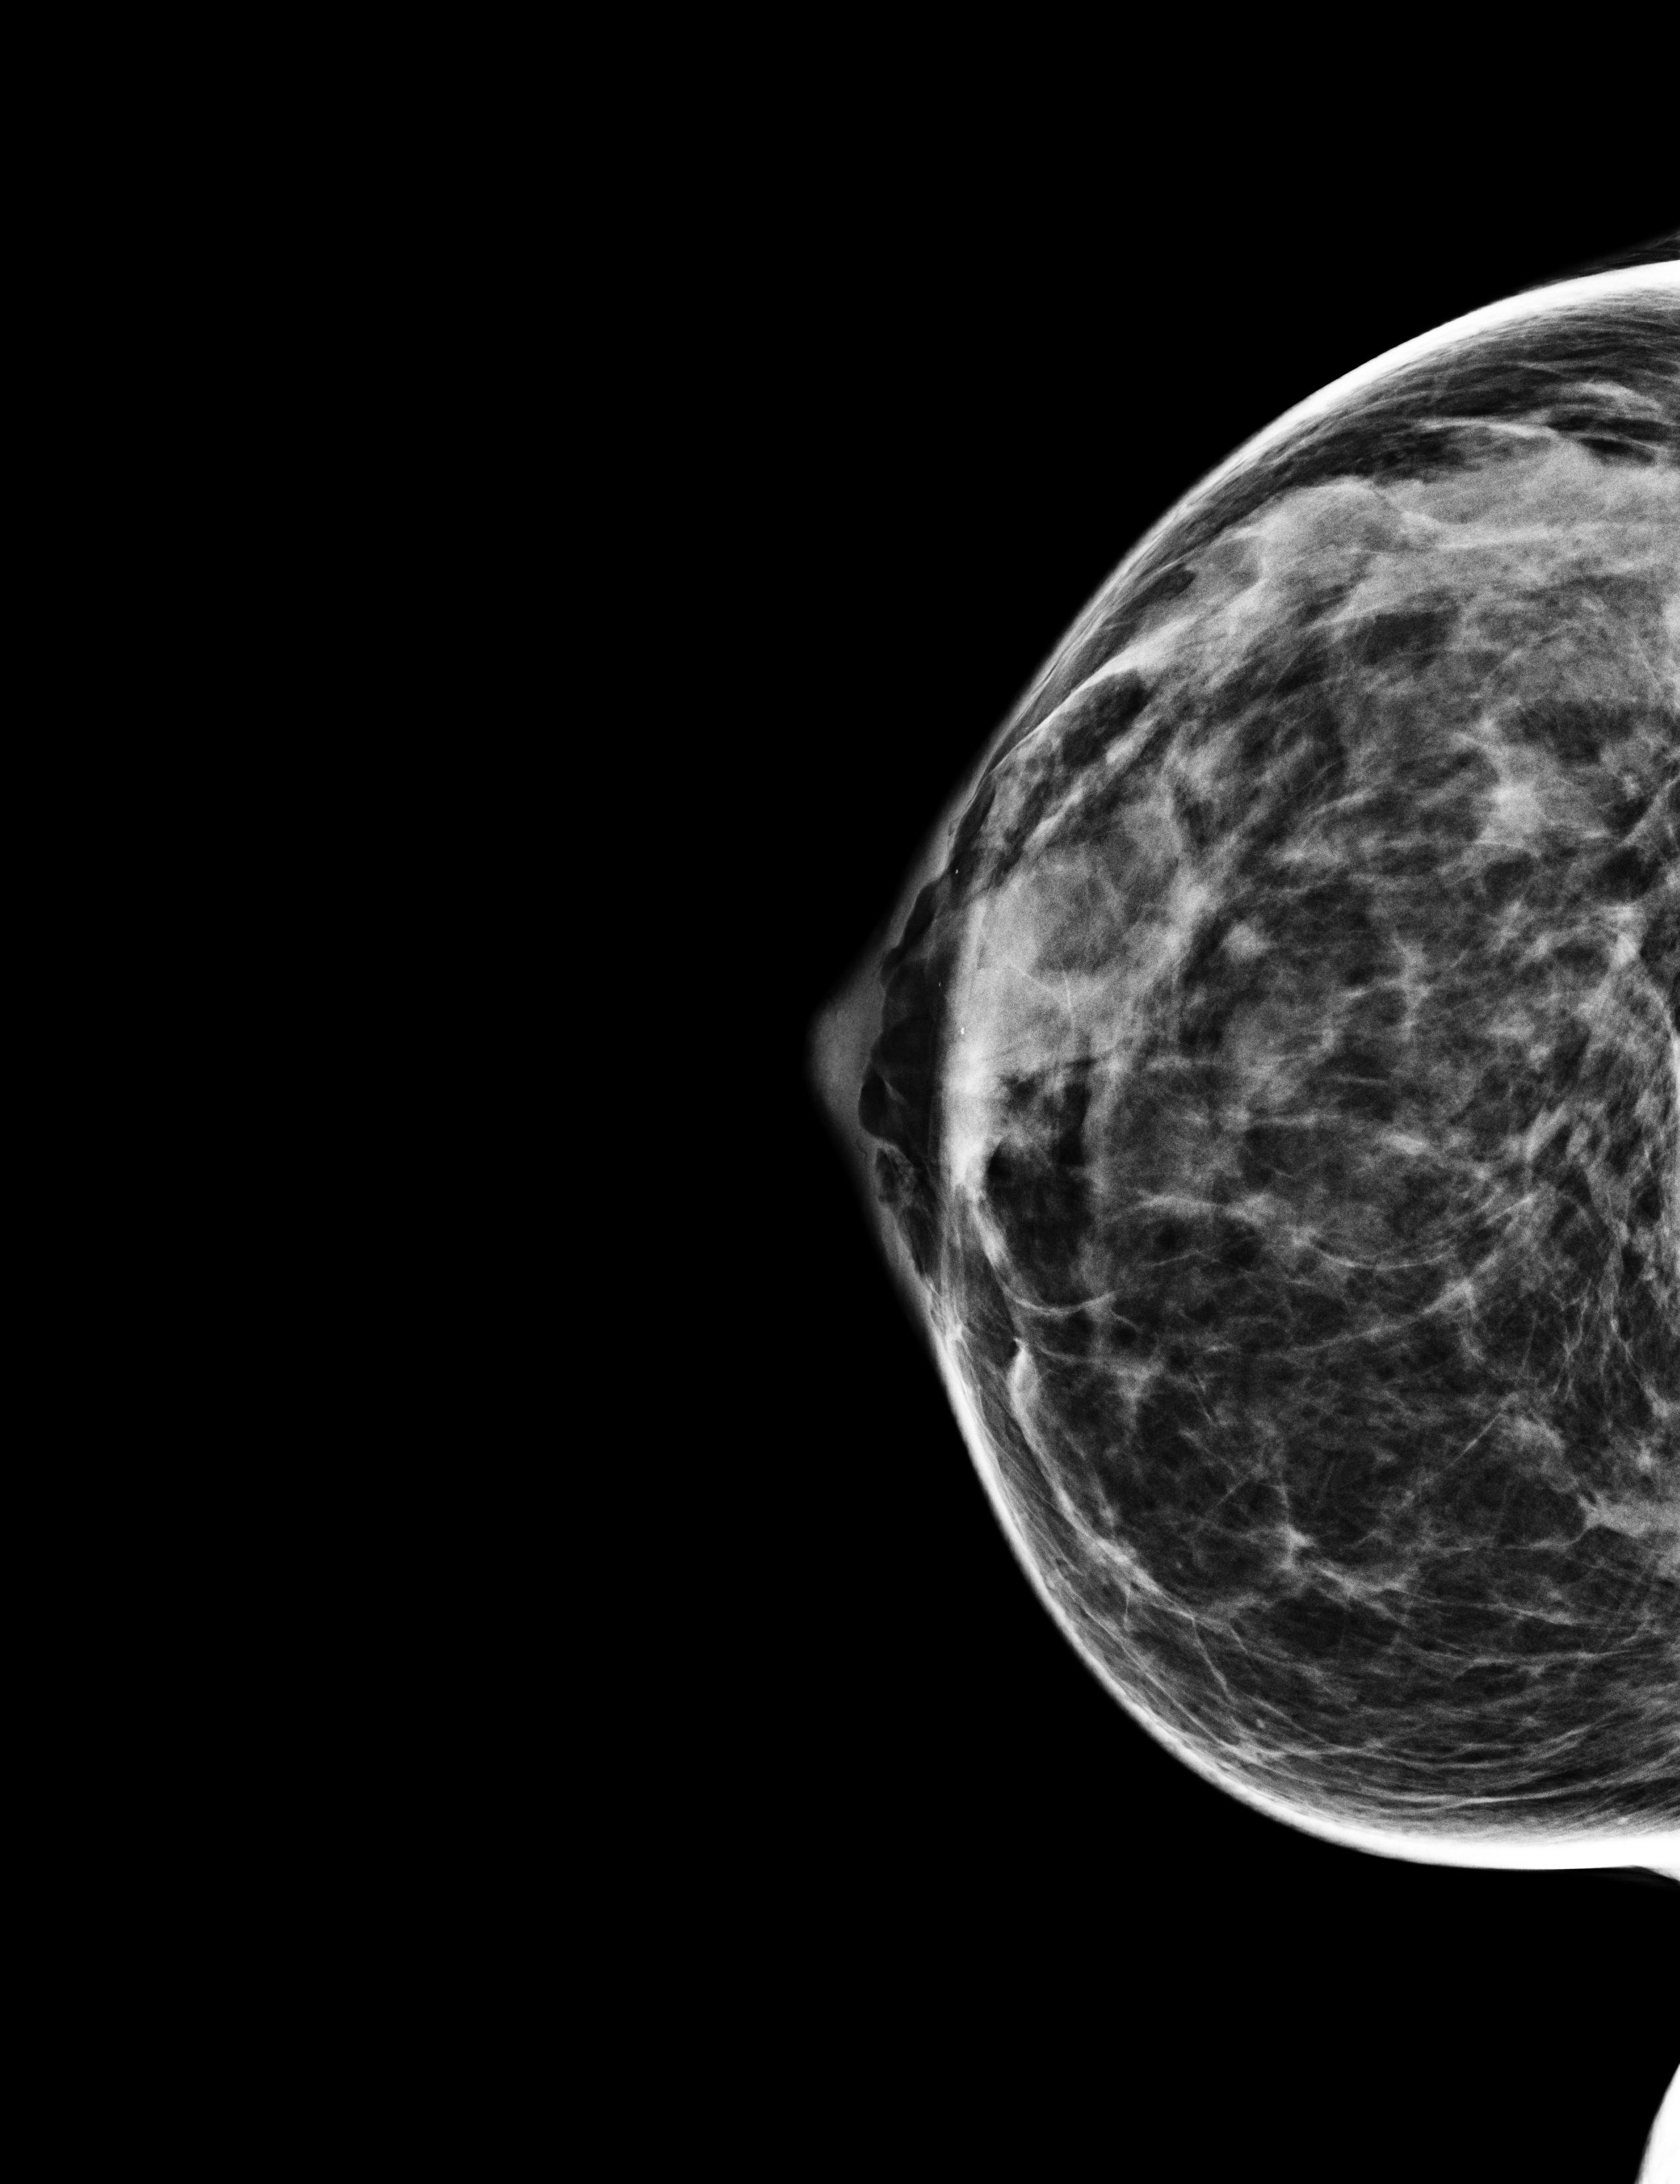
Full-field digital mammogram (FFDM); right breast; cranio-caudal projection; annual screening mammography examination; compressed breast thickness 46 mm. Patient: female, 44 years.
BI-RADS breast density category at the screening exam (both breasts, scale 1–4): 3. Final BI-RADS category for the screening round (tomosynthesis exam, both breasts): category 2. Recall: recalled for additional imaging after this screen.